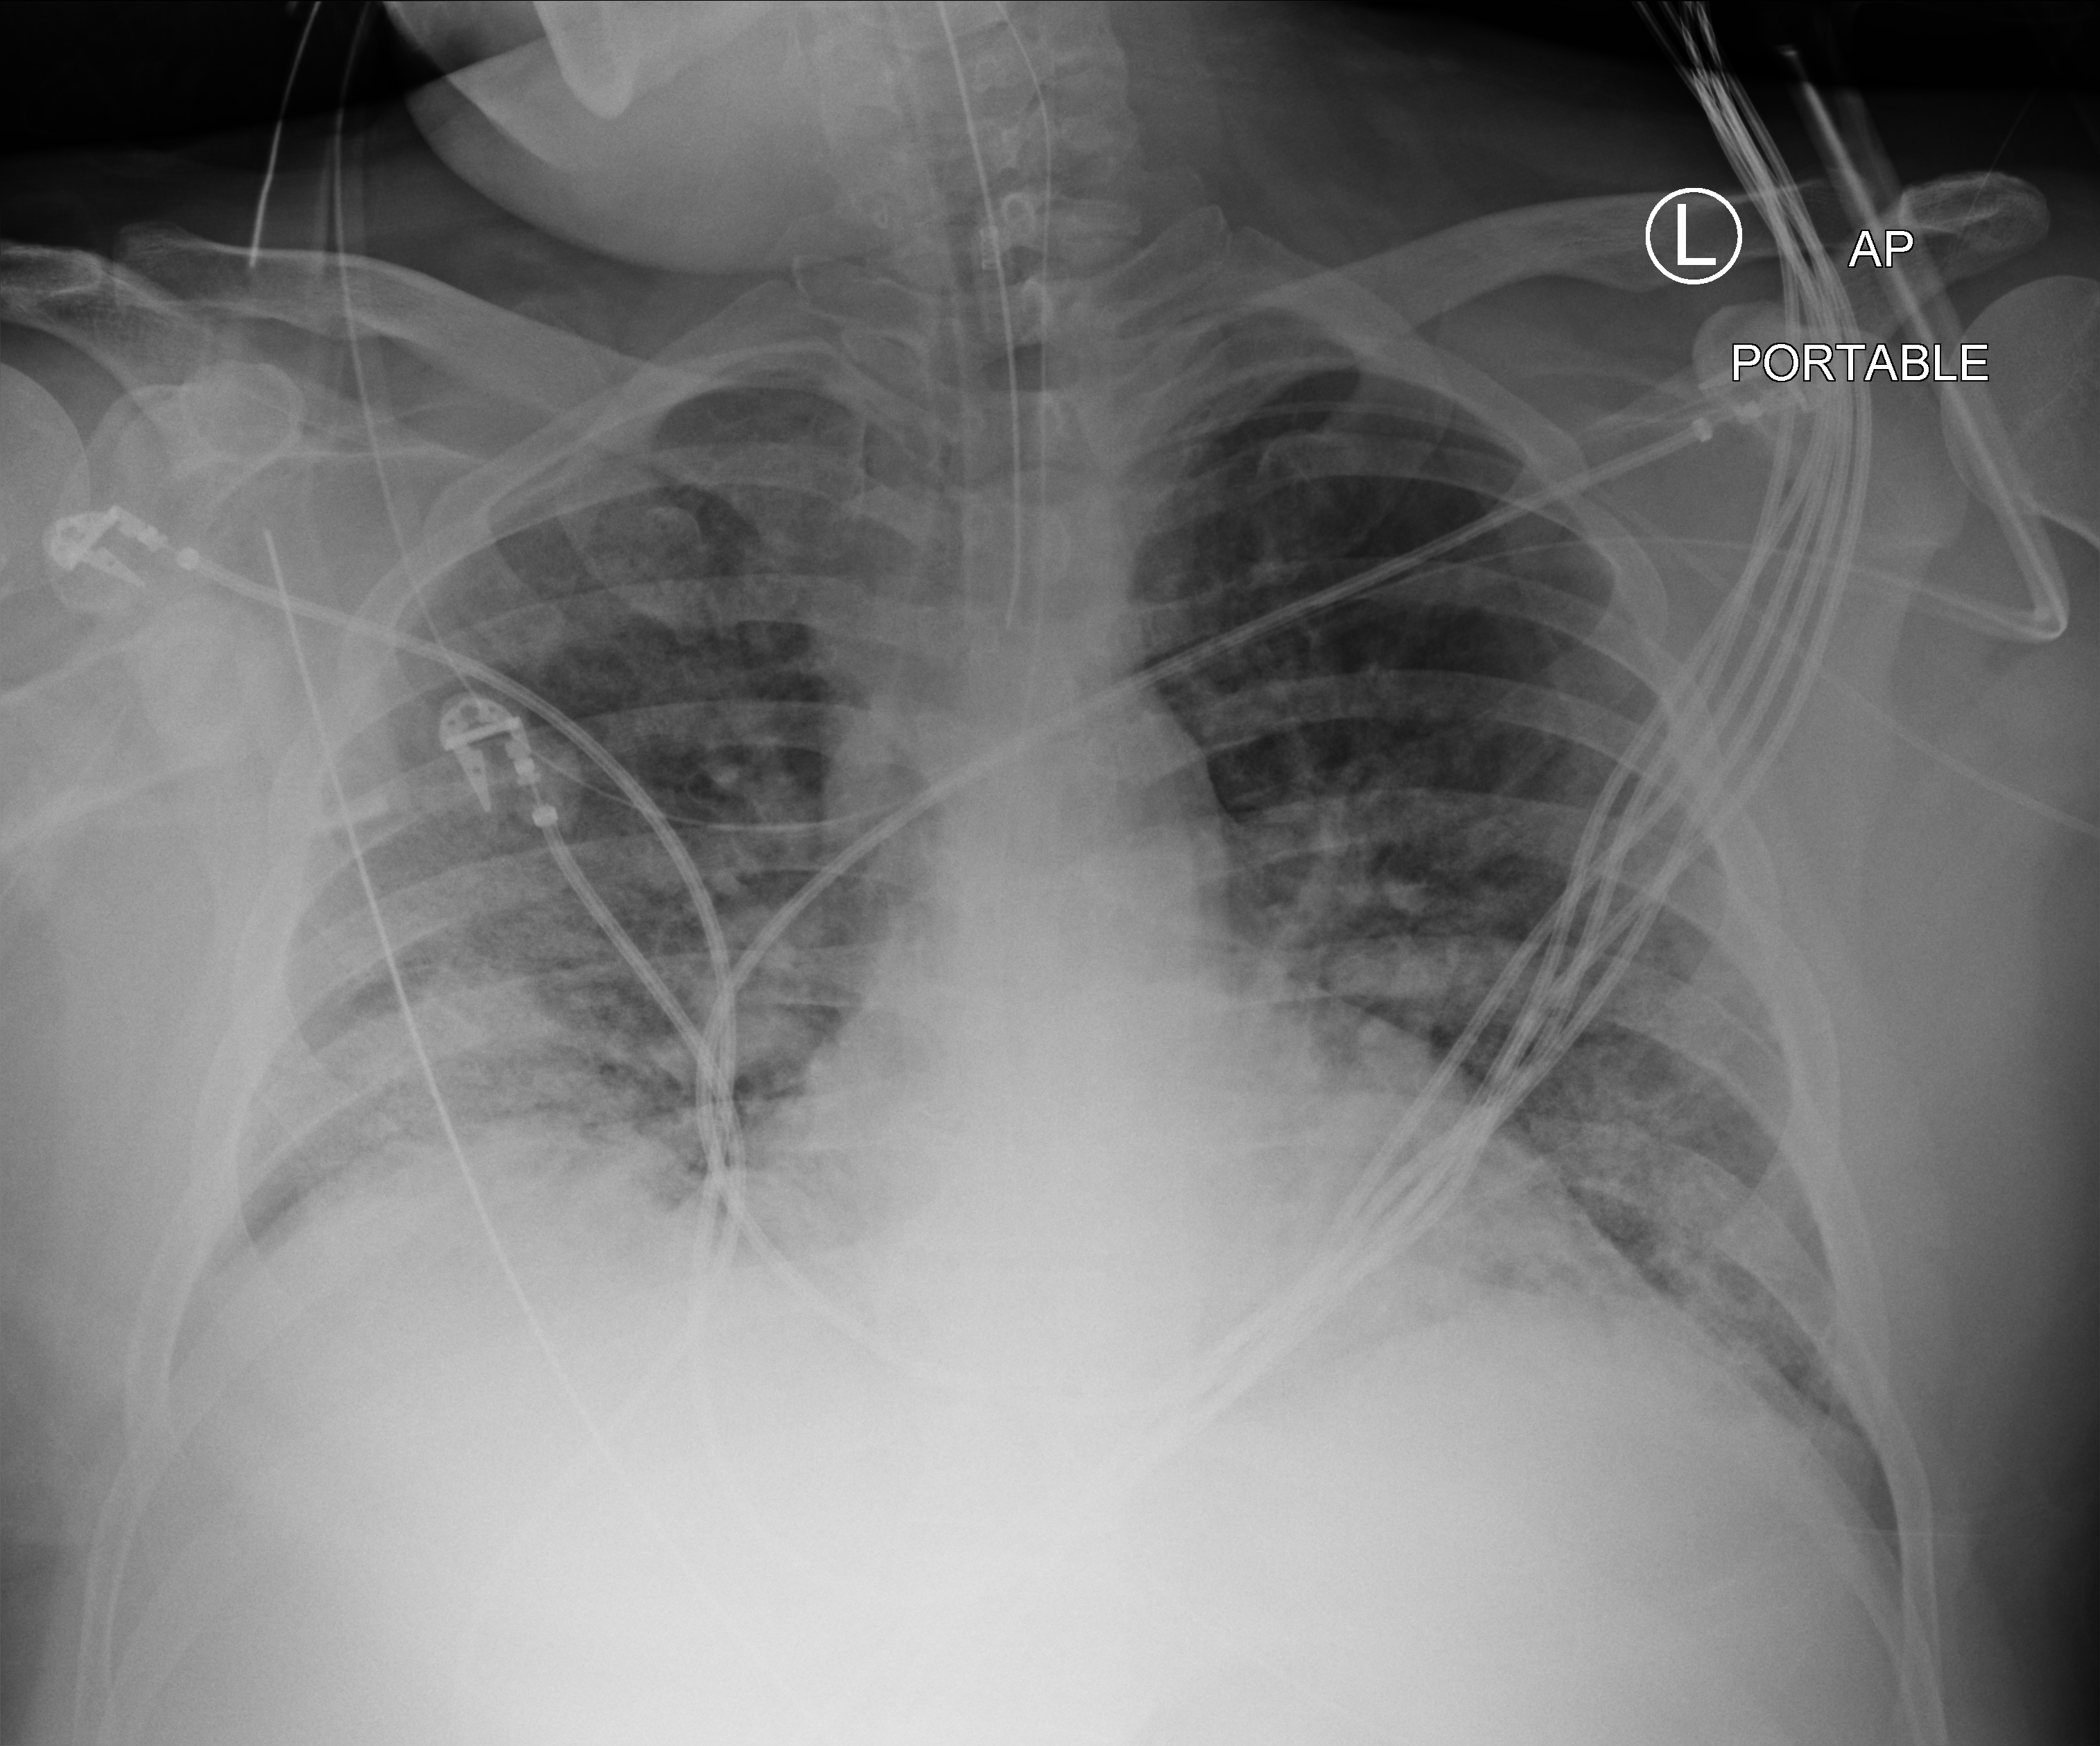
Chest X-ray (portable), anteroposterior (AP) projection. Patient hospitalised with COVID-19; male, aged 18–59 years.
Hospital-stay facts (about this admission, not read from this image; timing relative to this image not recorded): admitted to intensive care during this hospital stay: yes.